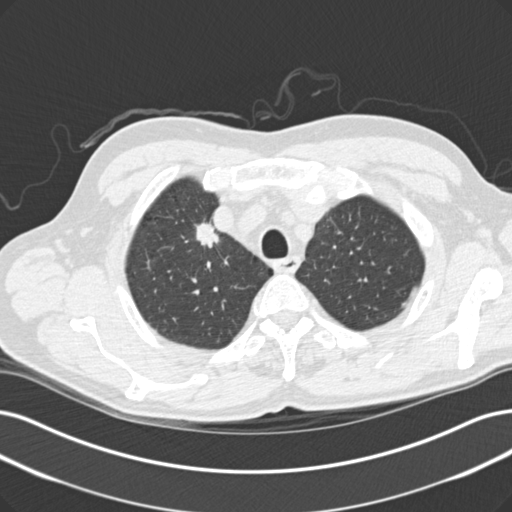
Low-dose screening chest CT, one axial slice. 120 kVp. Lung window (W 1500 / L -600 HU). 2 mm slice thickness. 512 × 512 image matrix.
Annotated regions visible in this slice (expert manual segmentation):
- lesion 1 (tumor, upper lobe of right lung): box from (x=195, y=221) to (x=219, y=248) px